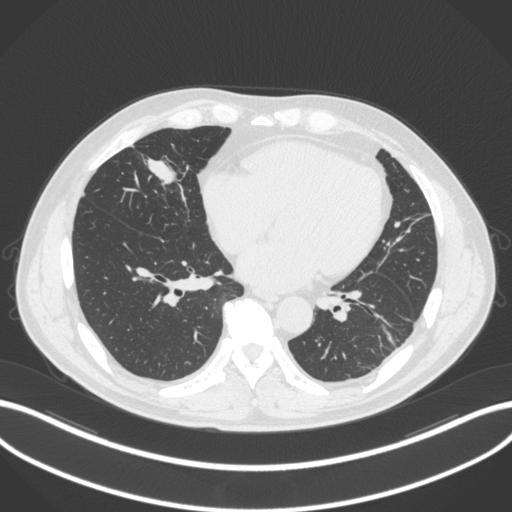
Chest CT, one axial slice. Slice 103 of 399 in the series (ordered by position). Reconstruction kernel B31f. Lung window (W 1500 / L -600 HU). 1 mm slice thickness. 512 × 512 image matrix. Patient: male, 59 years. From the clinical record (not read from this slice): clinical TNM (as recorded): T2a N1 M0.
Structures marked on this image (rectangle marked by the reading radiologist):
- lung tumour (recorded histology: adenocarcinoma): bounding box (x1, y1, x2, y2) in pixels: (143, 151, 190, 202)